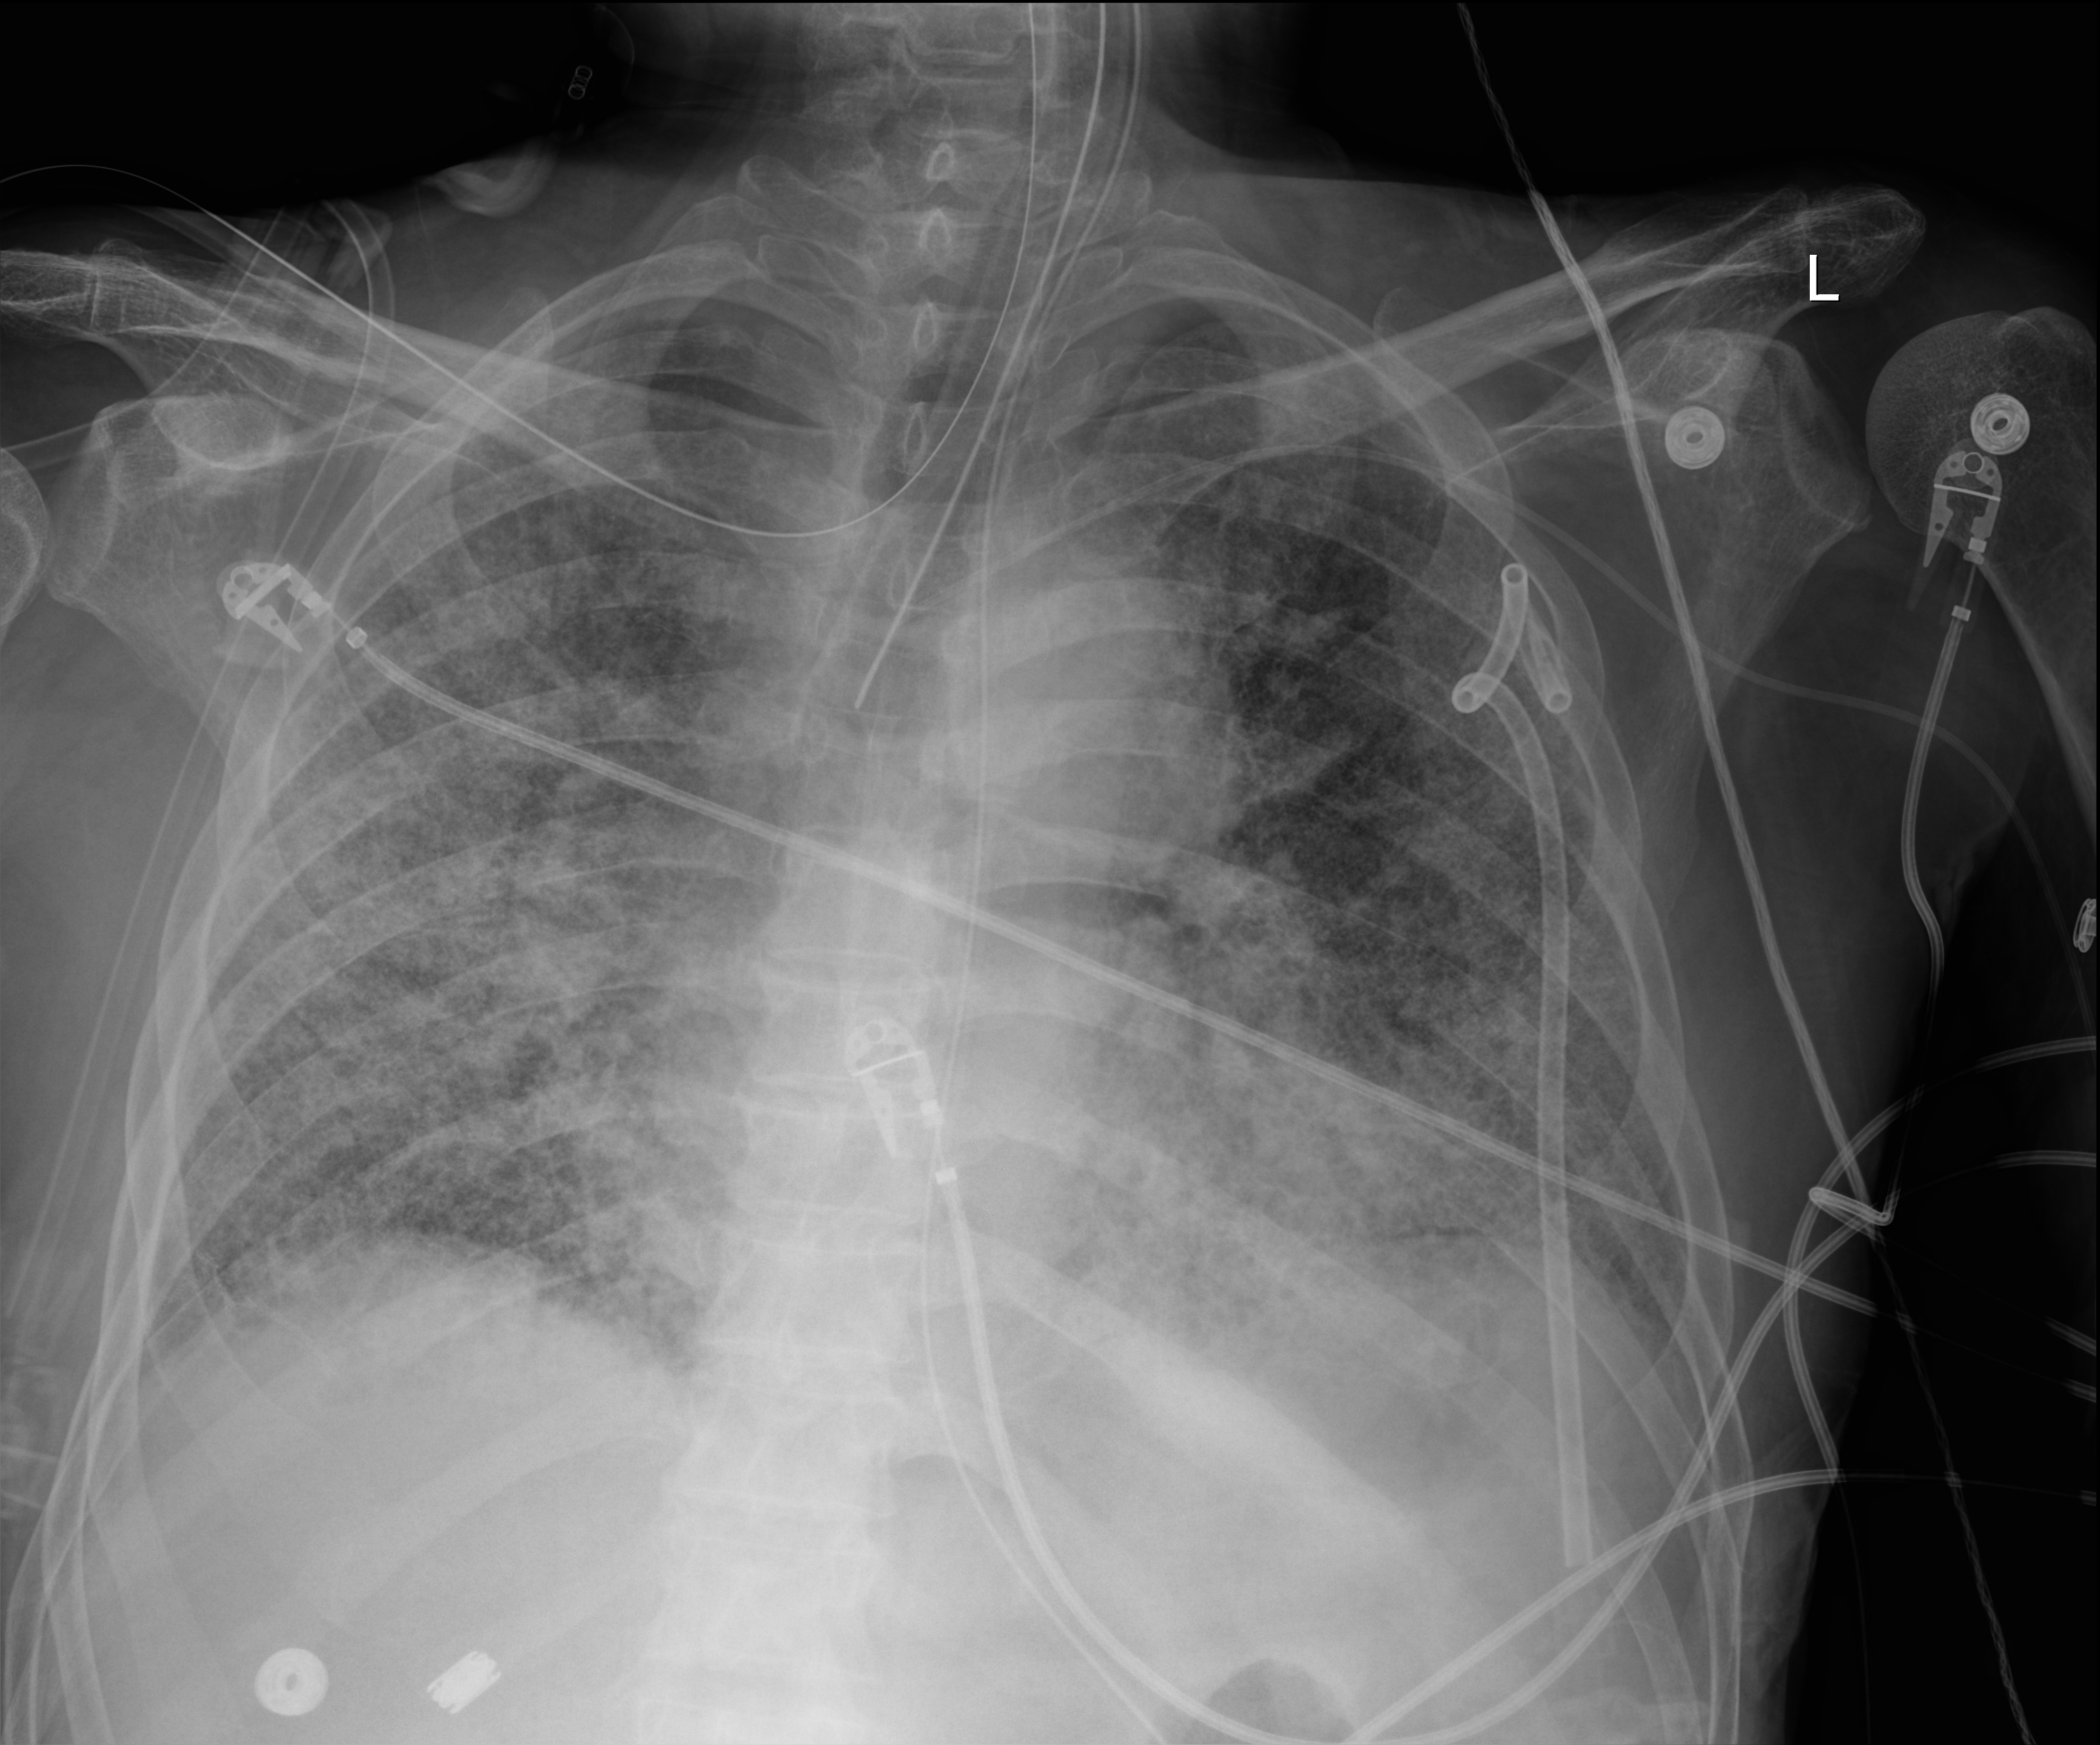
Chest radiograph; anteroposterior (AP) projection. Male patient hospitalised with COVID-19, age 60–74 years.
From the hospital-stay record, not from the radiograph (when in the stay this image was taken is not recorded):
- length of hospital stay: 54 days